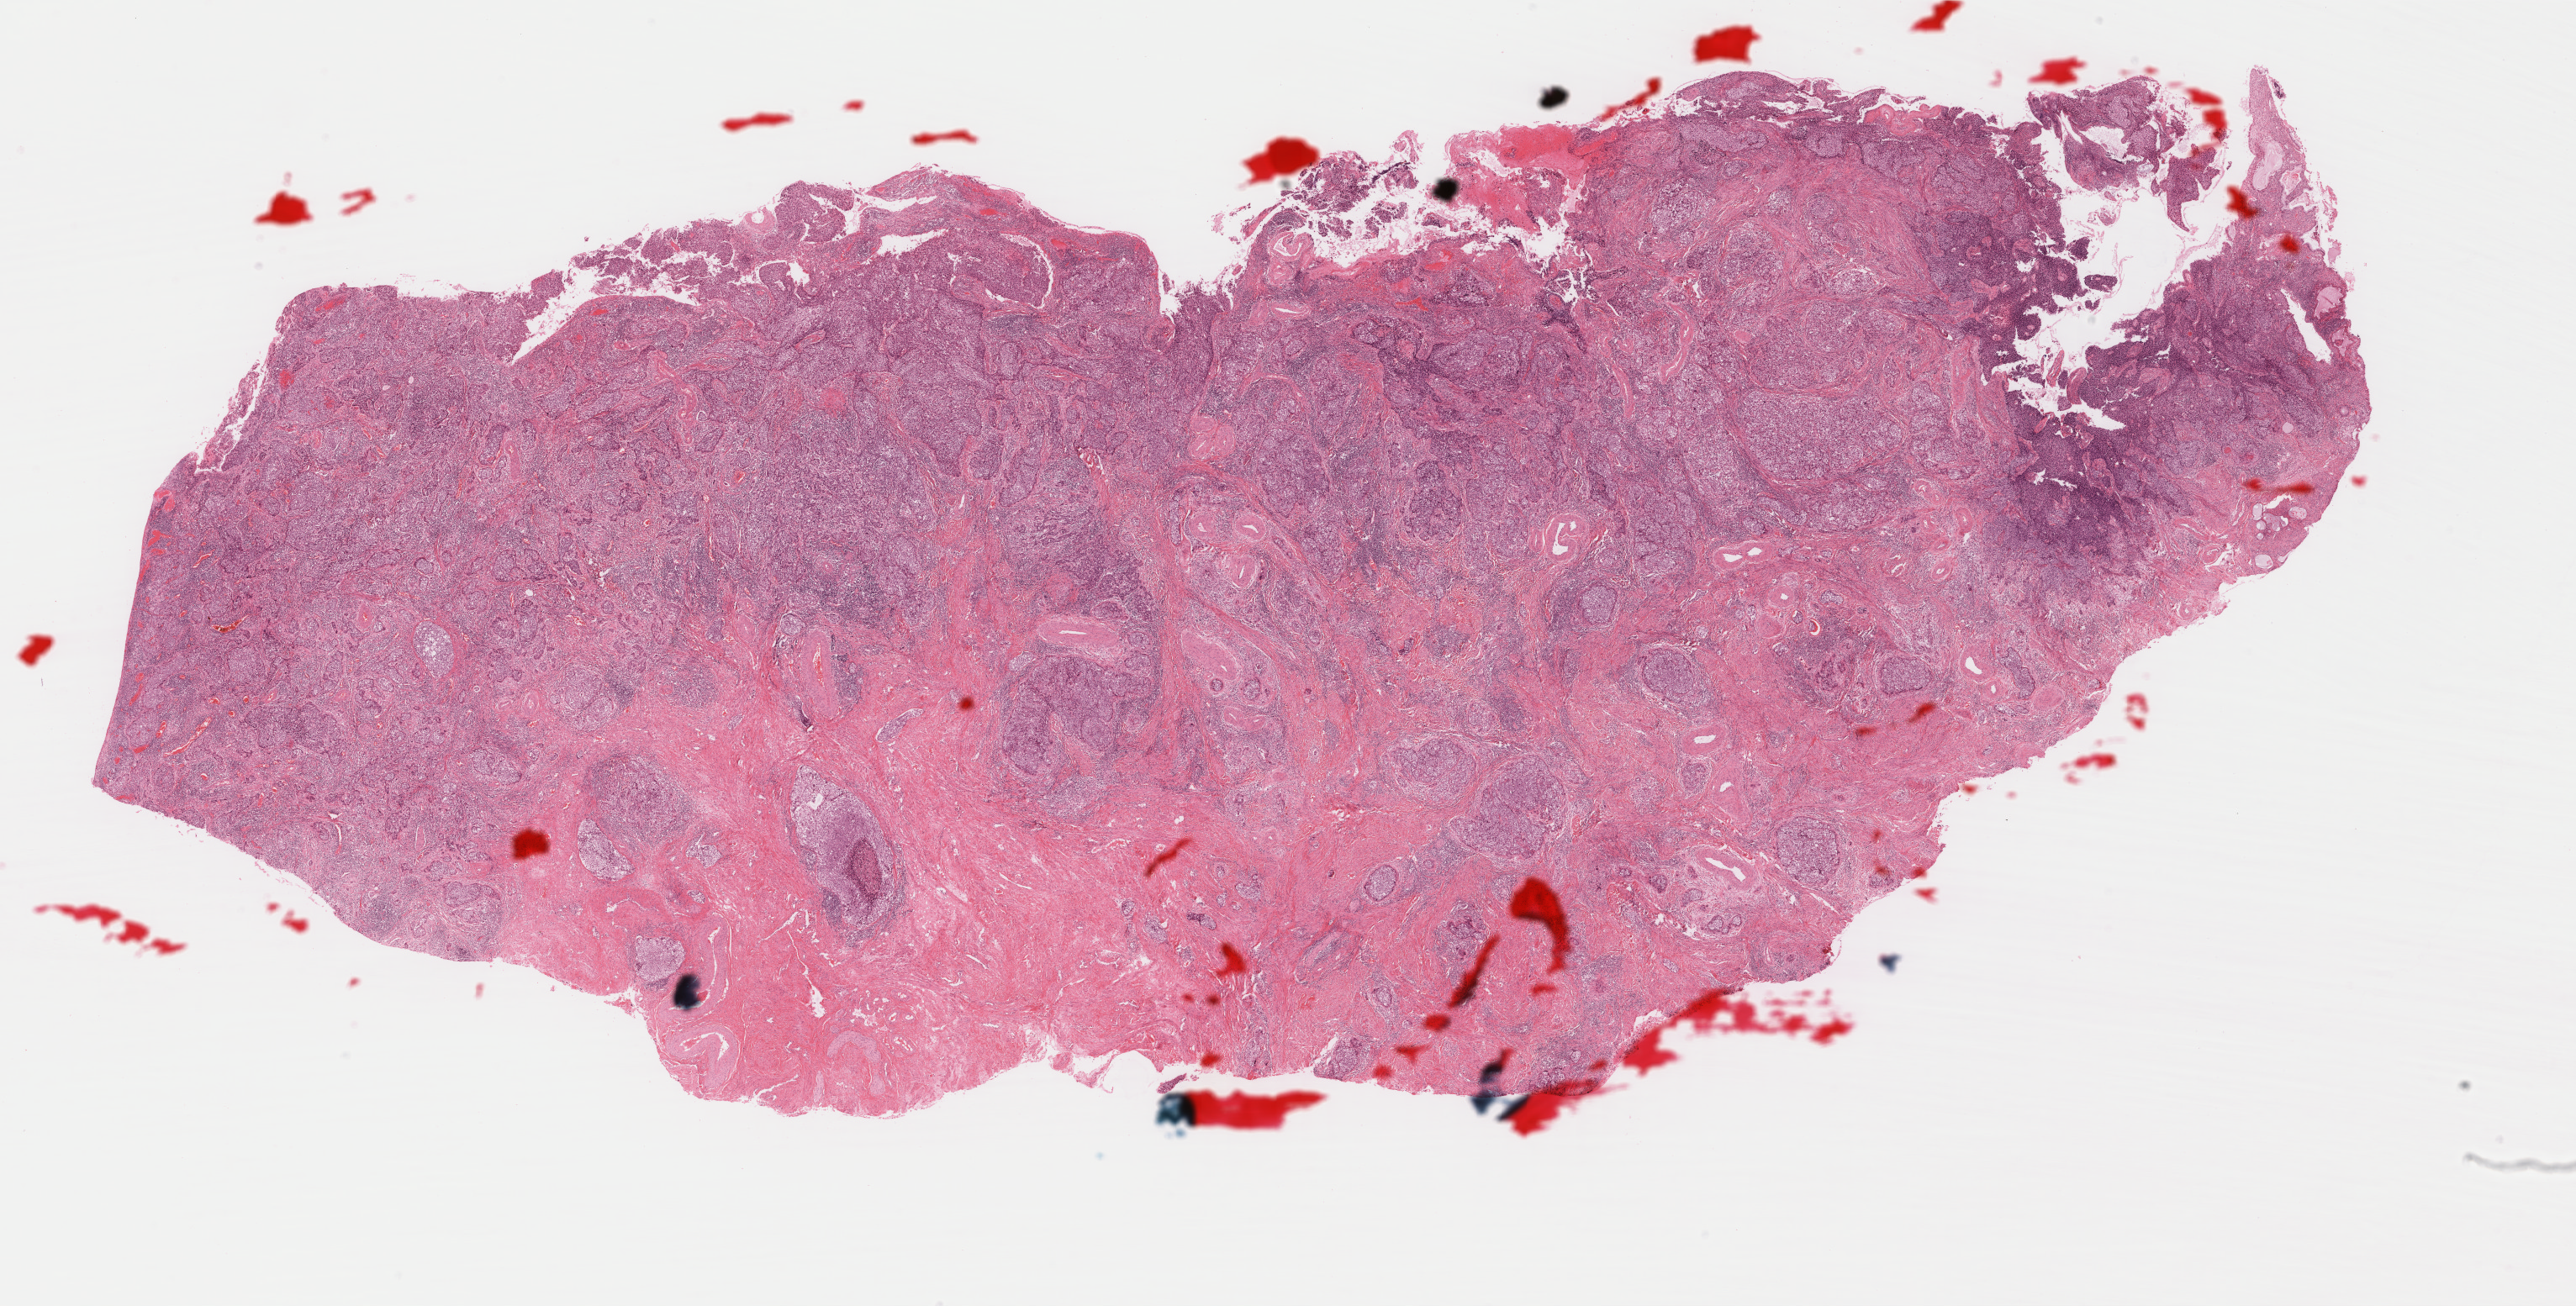
Digitized Hematoxylin and eosin (H&E) stained tissue section (whole slide), a low-resolution overview of the entire scanned area, about 24.3 x 12.3 mm (slide scanned at 40x); formalin-fixed paraffin-embedded (FFPE) diagnostic section; sample: primary tumour, cervix. Female patient; age at initial diagnosis 59 years. Histologic grade: G3 (poorly differentiated).
FIGO stage: IIIB. Pathologic diagnosis: Squamous cell carcinoma, NOS. Lymph nodes positive (case pathology): 1 of 6 examined.